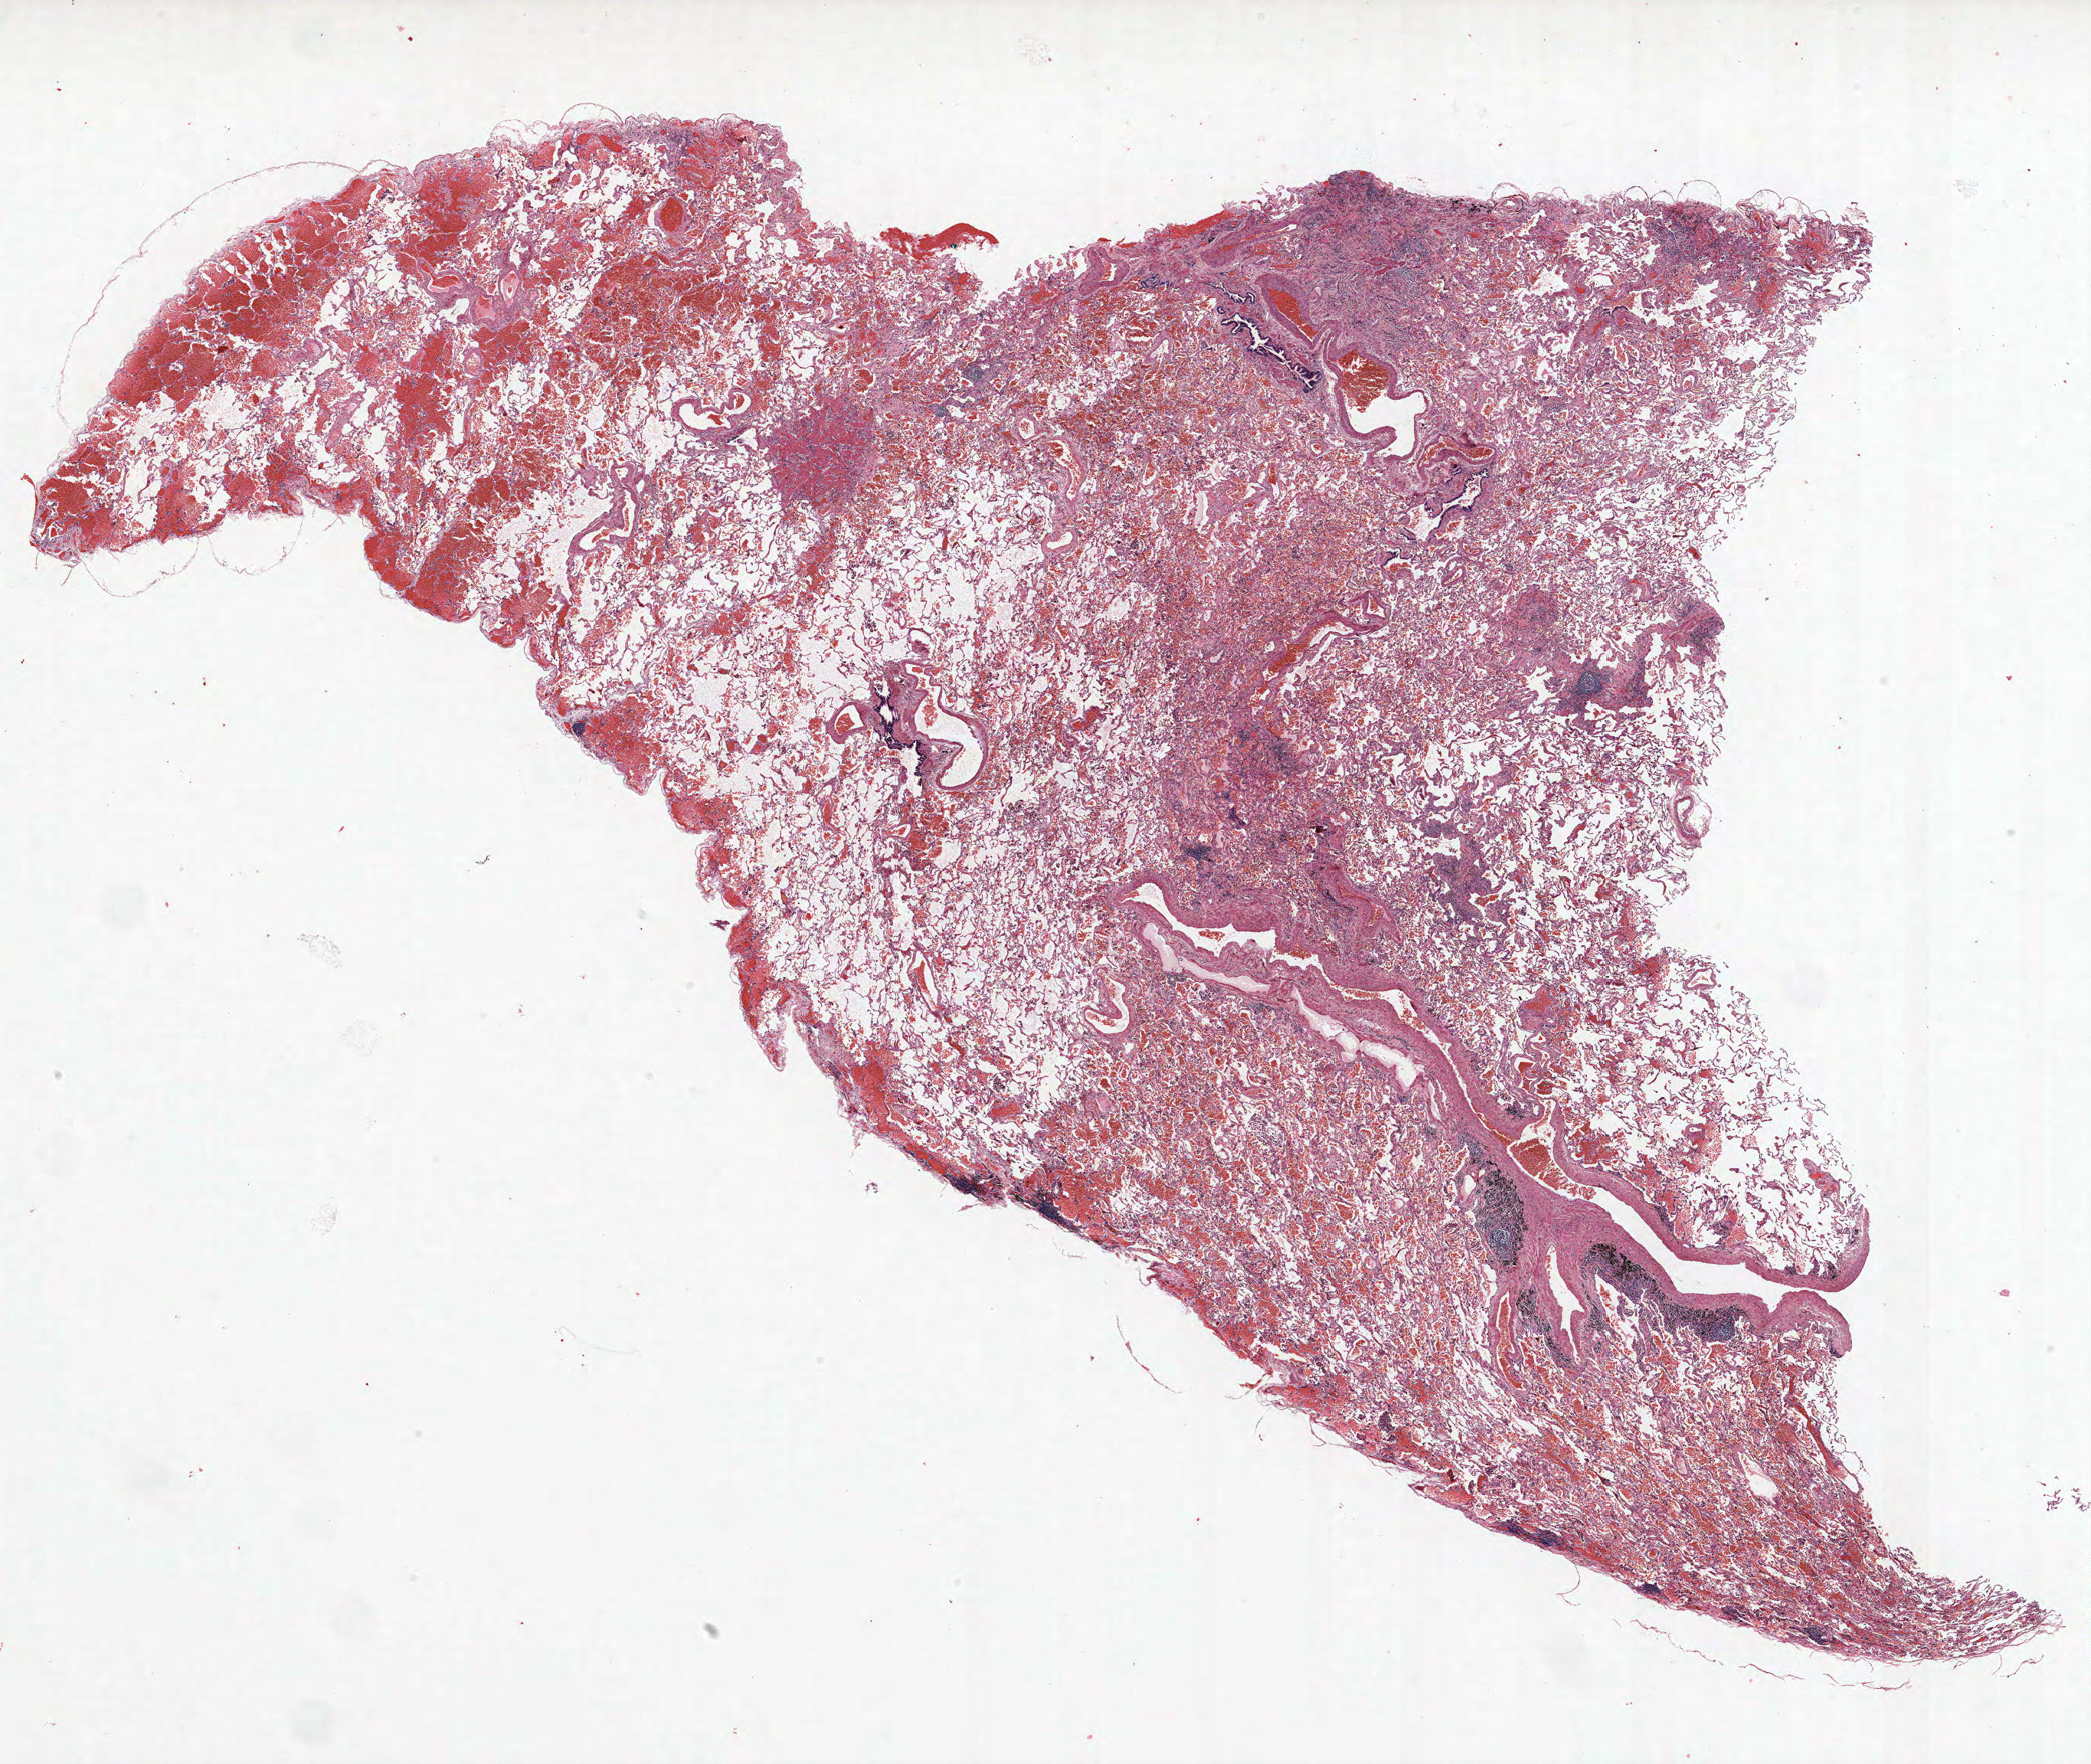
Hematoxylin and eosin (H&E) stained whole-slide image, shown as a low-resolution overview of the whole scanned area (about 21.8 x 18.4 mm), formalin-fixed paraffin-embedded (FFPE) section, lung. Male, age 68 at enrolment. Current smoker at enrolment. Grade: moderately differentiated (G2).
Stage (AJCC 6th edition): IB. Participant's lung-cancer diagnosis: Squamous cell carcinoma, NOS. Tumour size (pathology): 20 mm. Primary tumour location (clinical record): right lower lobe.